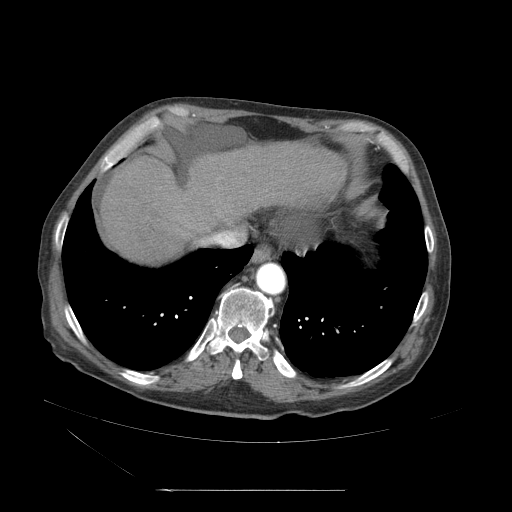
Contrast-enhanced abdominal CT (liver protocol), one axial slice. Position 52 of 71 along the scan axis. Reconstruction kernel STANDARD. 120 kVp. Soft-tissue window (W 400 / L 40 HU). 2.5 mm slice thickness. 512 × 512 image matrix, field of view 440 × 440 mm. From the clinical record (not read from this slice): diagnosis: hepatocellular carcinoma (patient treated with transarterial chemoembolisation; whether this scan precedes or follows treatment is not stated here); TNM stage (as recorded): Stage-II; Child-Pugh class: A; tumour size: 1 cm.
Annotated regions visible in this slice (semi-automatic segmentation, software-assisted and operator-edited):
- abdominal aorta: bounding box <256,263,286,295> (left, top, right, bottom; pixels)
- liver parenchyma outside the tumour (the mass and vessels are separate outlines, so this box may not span the whole liver): <102,140,335,265>
- liver vessels: <115,197,248,254>